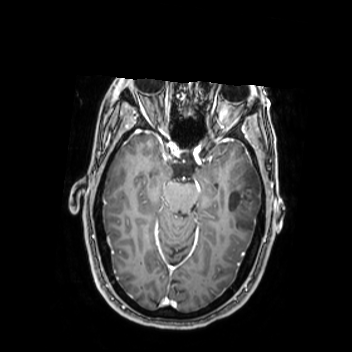
Brain MRI from a brain-tumour surgery series, one axial slice. Slice 163 of 350 in the series (ordered by position). T1-weighted post-contrast. 0.9 mm slice thickness. 352 × 352 image matrix, field of view 280 × 280 mm. From the clinical record (not read from this slice): histopathology: Oligodendroglioma; WHO grade: 2; IDH mutation: yes; tumour location: Left Middle Temporal Gyrus.
Annotated regions visible in this slice (expert manual segmentation):
- tumour: box from (x=224, y=163) to (x=262, y=236) px